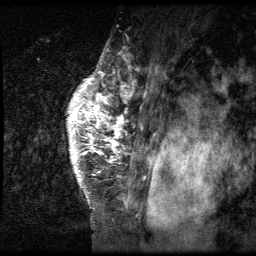
Breast MRI (dynamic contrast-enhanced), one sagittal slice. Position 51 of 64 along the scan axis. 3 images stored at this slice position (order not interpretable as contrast timing). 1.5 T. TE 4.2 ms, TR 9 ms. 2.5 mm slice thickness. 256 × 256 image matrix. Patient: female, 50 years. Case-level facts recorded for this patient, not image findings: setting: breast cancer imaged before/during neoadjuvant chemotherapy; receptor status: triple-negative.
Annotated regions visible in this slice (semi-automatic segmentation, software-assisted and operator-edited):
- analysis volume of interest (the breast-tissue region the enhancement analysis was run in; not a lesion): bounding box <27,39,137,212> (left, top, right, bottom; pixels)
- tumour enhancement mask (voxels above the 140 % enhancement threshold inside the analysis volume of interest): <68,65,137,207>